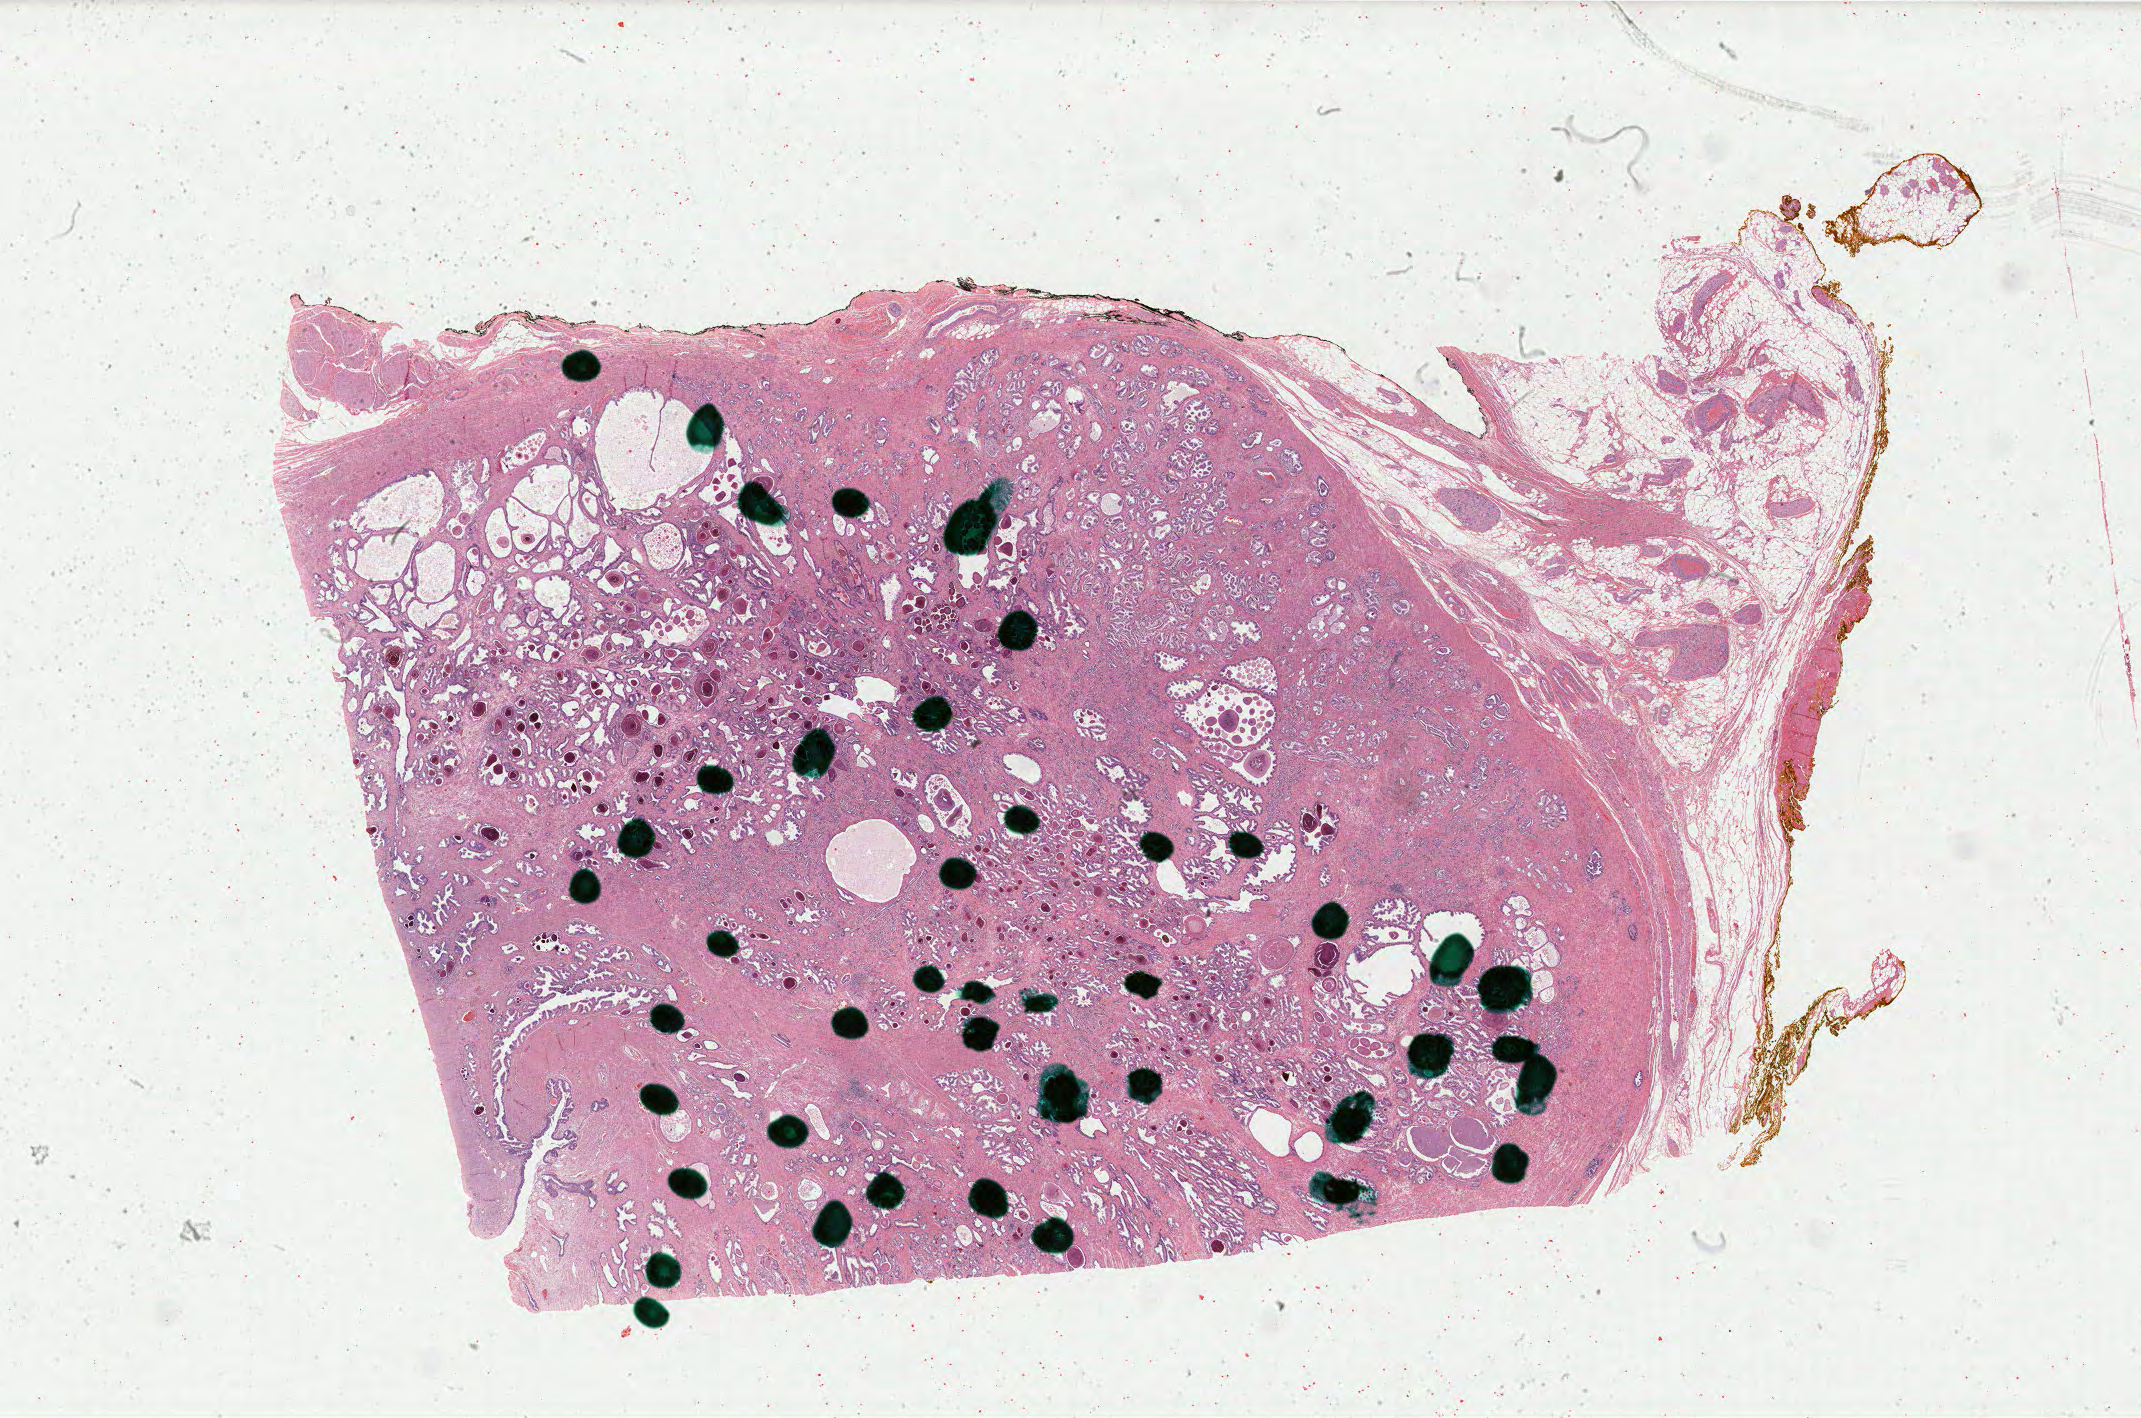
Whole-slide histology image, Hematoxylin and eosin (H&E) stained — low-resolution overview of the scanned area, about 34.0 x 22.5 mm (slide scanned at 40x); formalin-fixed paraffin-embedded (FFPE) diagnostic section; sample: primary tumour, prostate. Male, age 55 years at initial diagnosis. Gleason score: 7 (3+4).
- diagnosis: Adenocarcinoma, NOS (prostate gland)